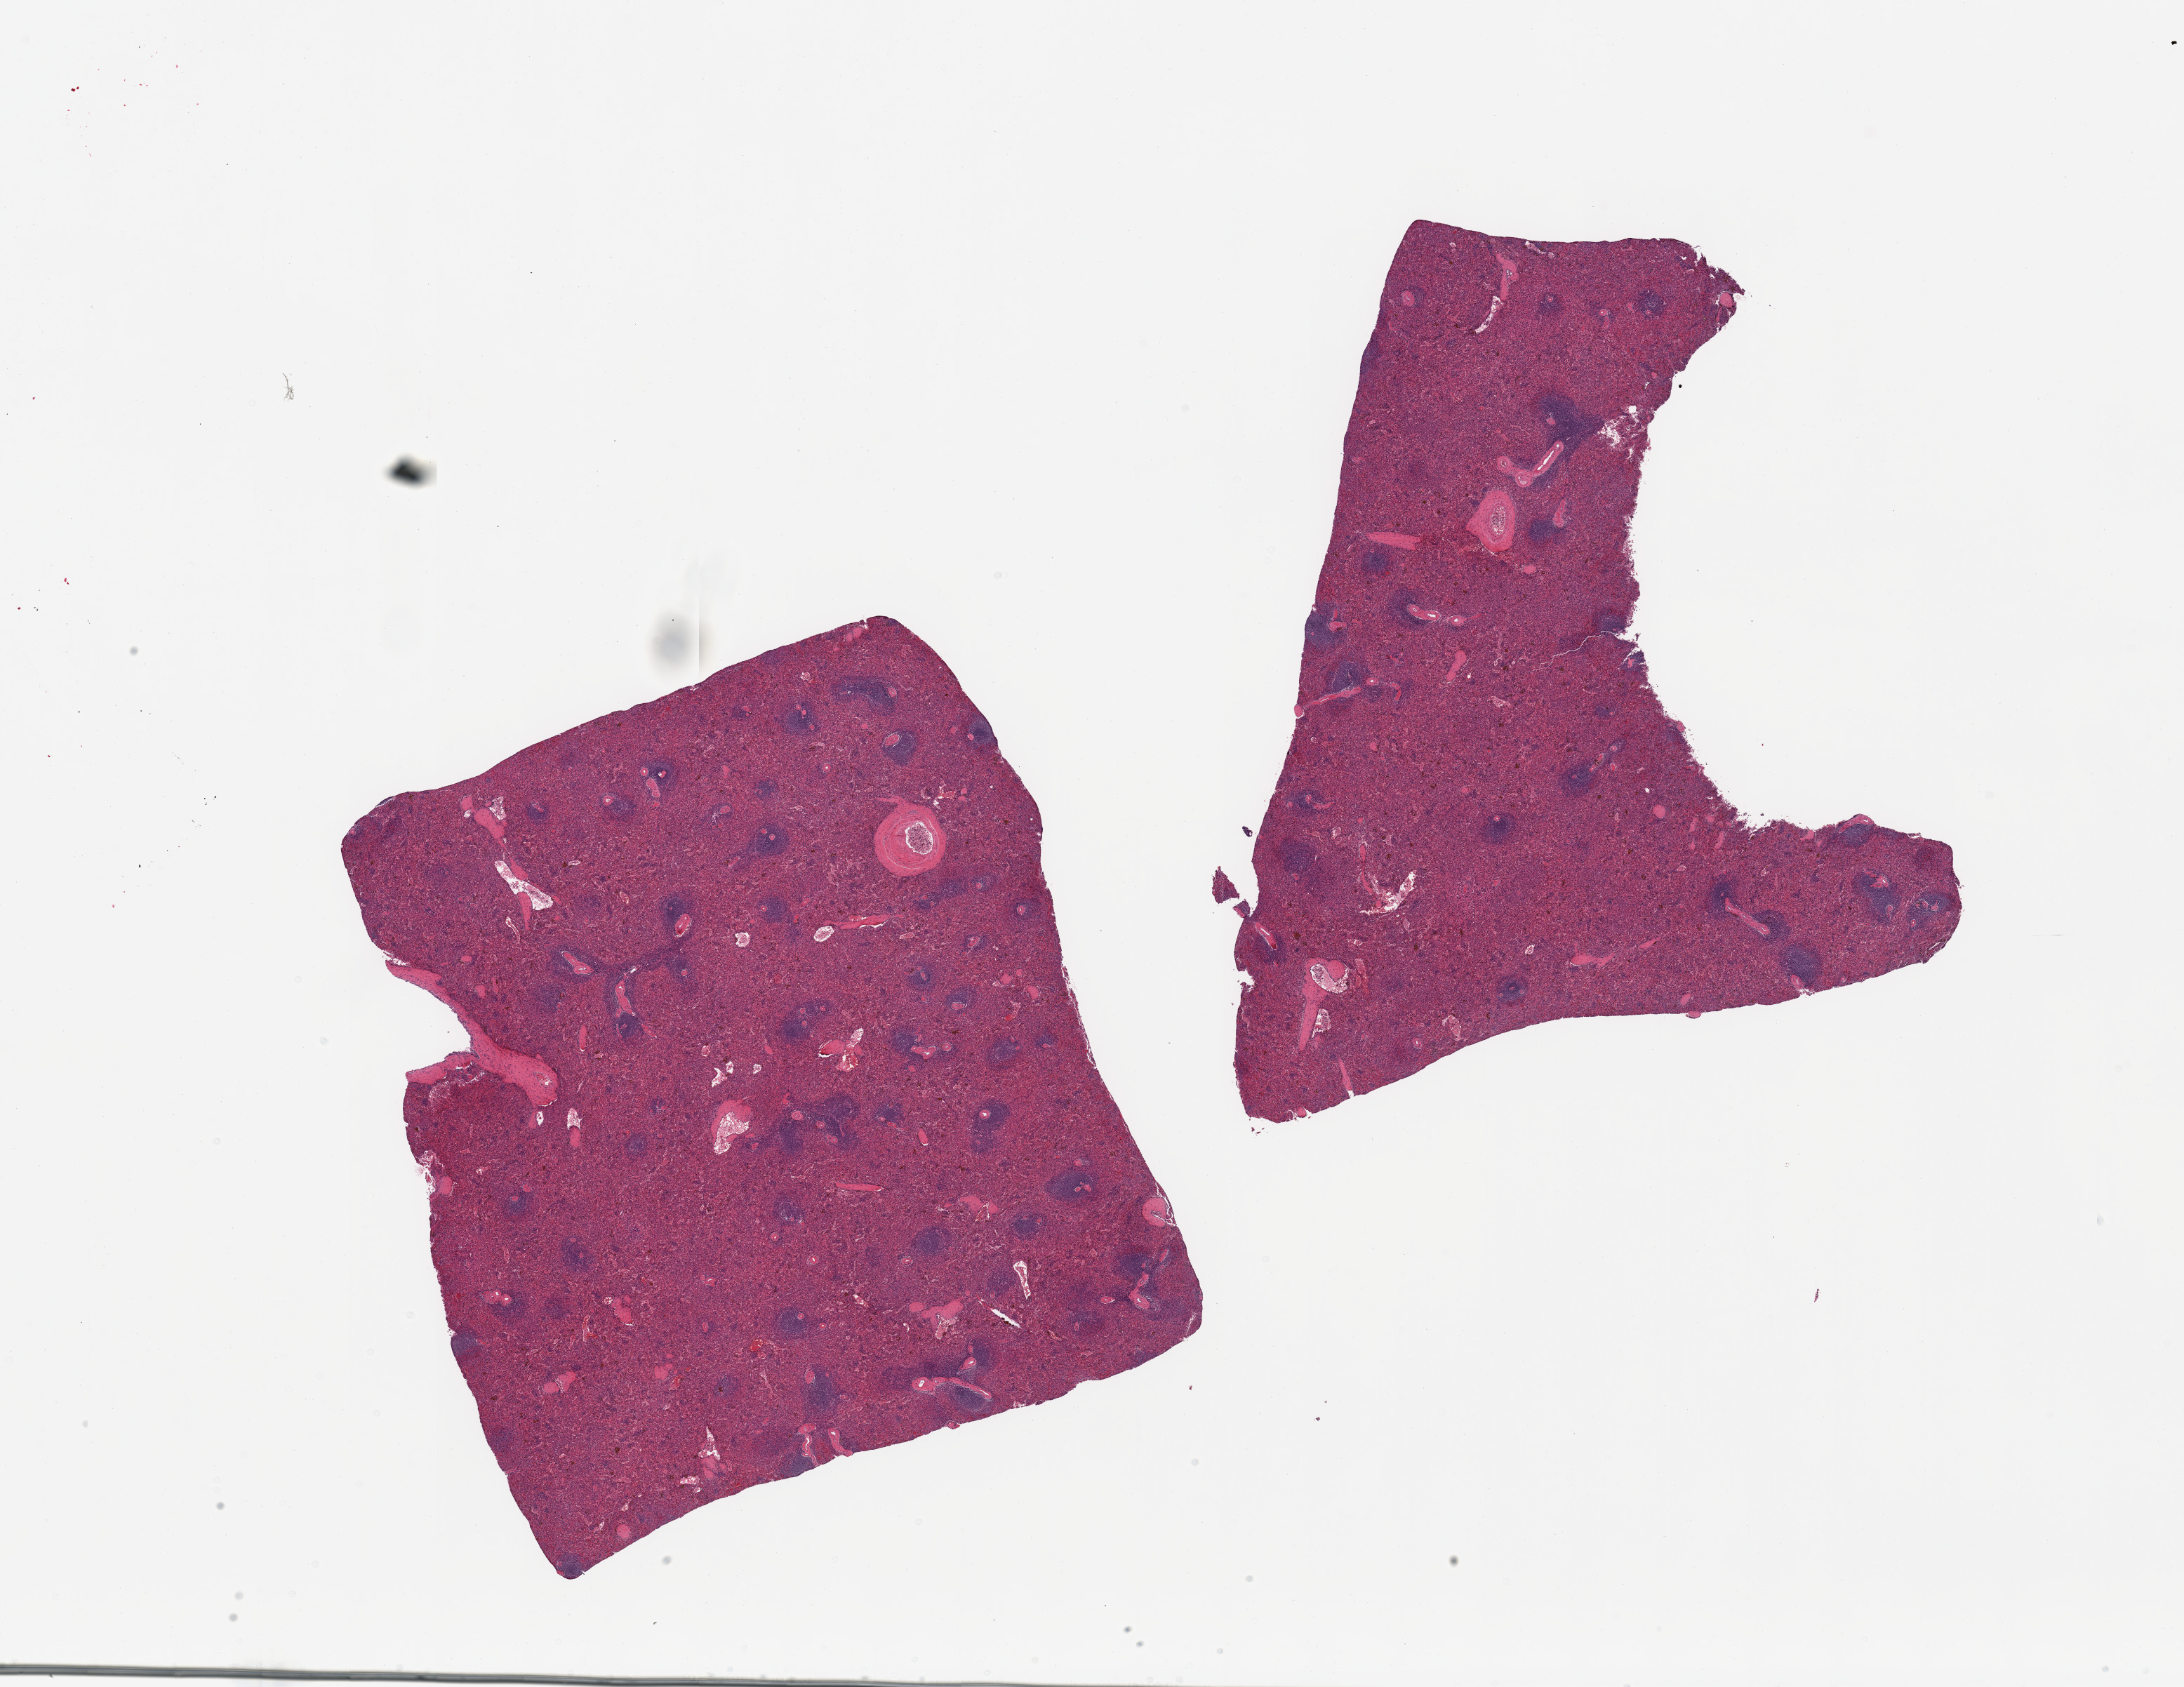
Whole-slide image, H&E stain, a low-resolution overview of the entire scanned area, about 24.6 x 19.0 mm. PAXgene-fixed paraffin-embedded (PFPE) section. Sampled site (target tissue): spleen. Donor tissue sample.
Pathologist's review note for this sample: 2 pieces, mild congestion.